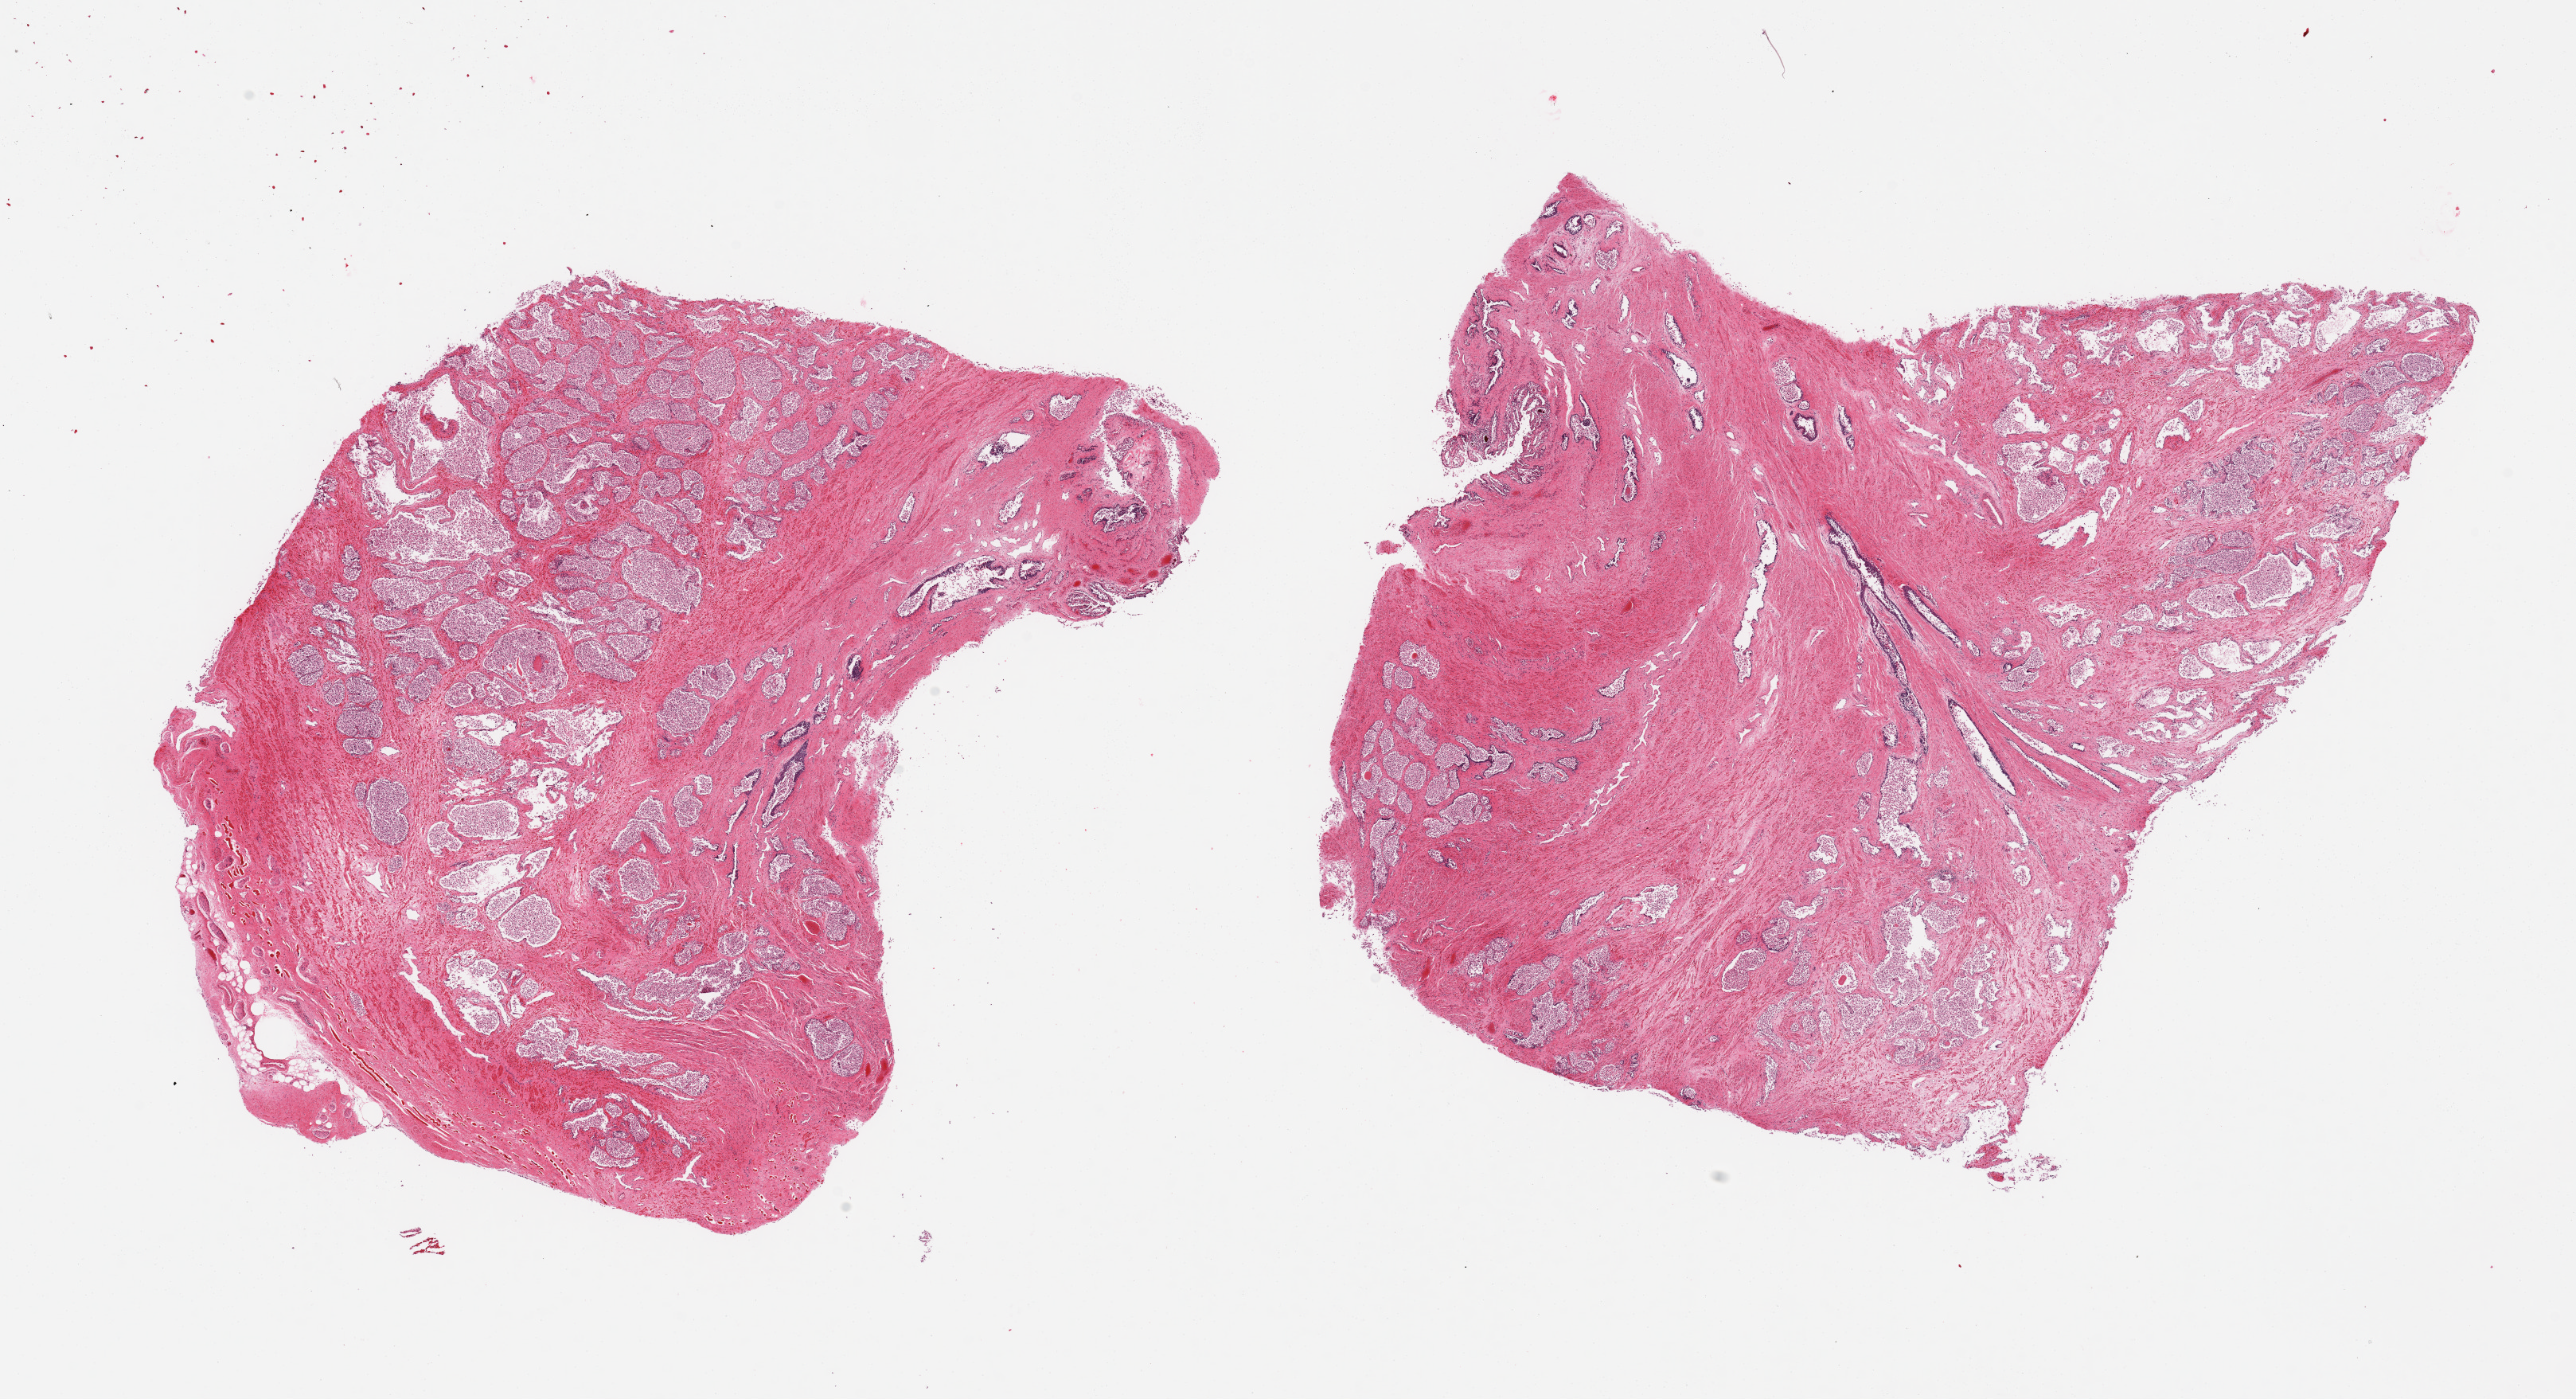
Hematoxylin and eosin (H&E) whole-slide image, brightfield, a low-resolution overview of the entire scanned area, about 25.6 x 13.9 mm. PAXgene-fixed, paraffin-embedded tissue. Sampled site (target tissue): prostate. Donor tissue sample. Male donor.
Pathologist's review note for this sample: 2 pieces, glandular component with advanced mucosal autolysis.